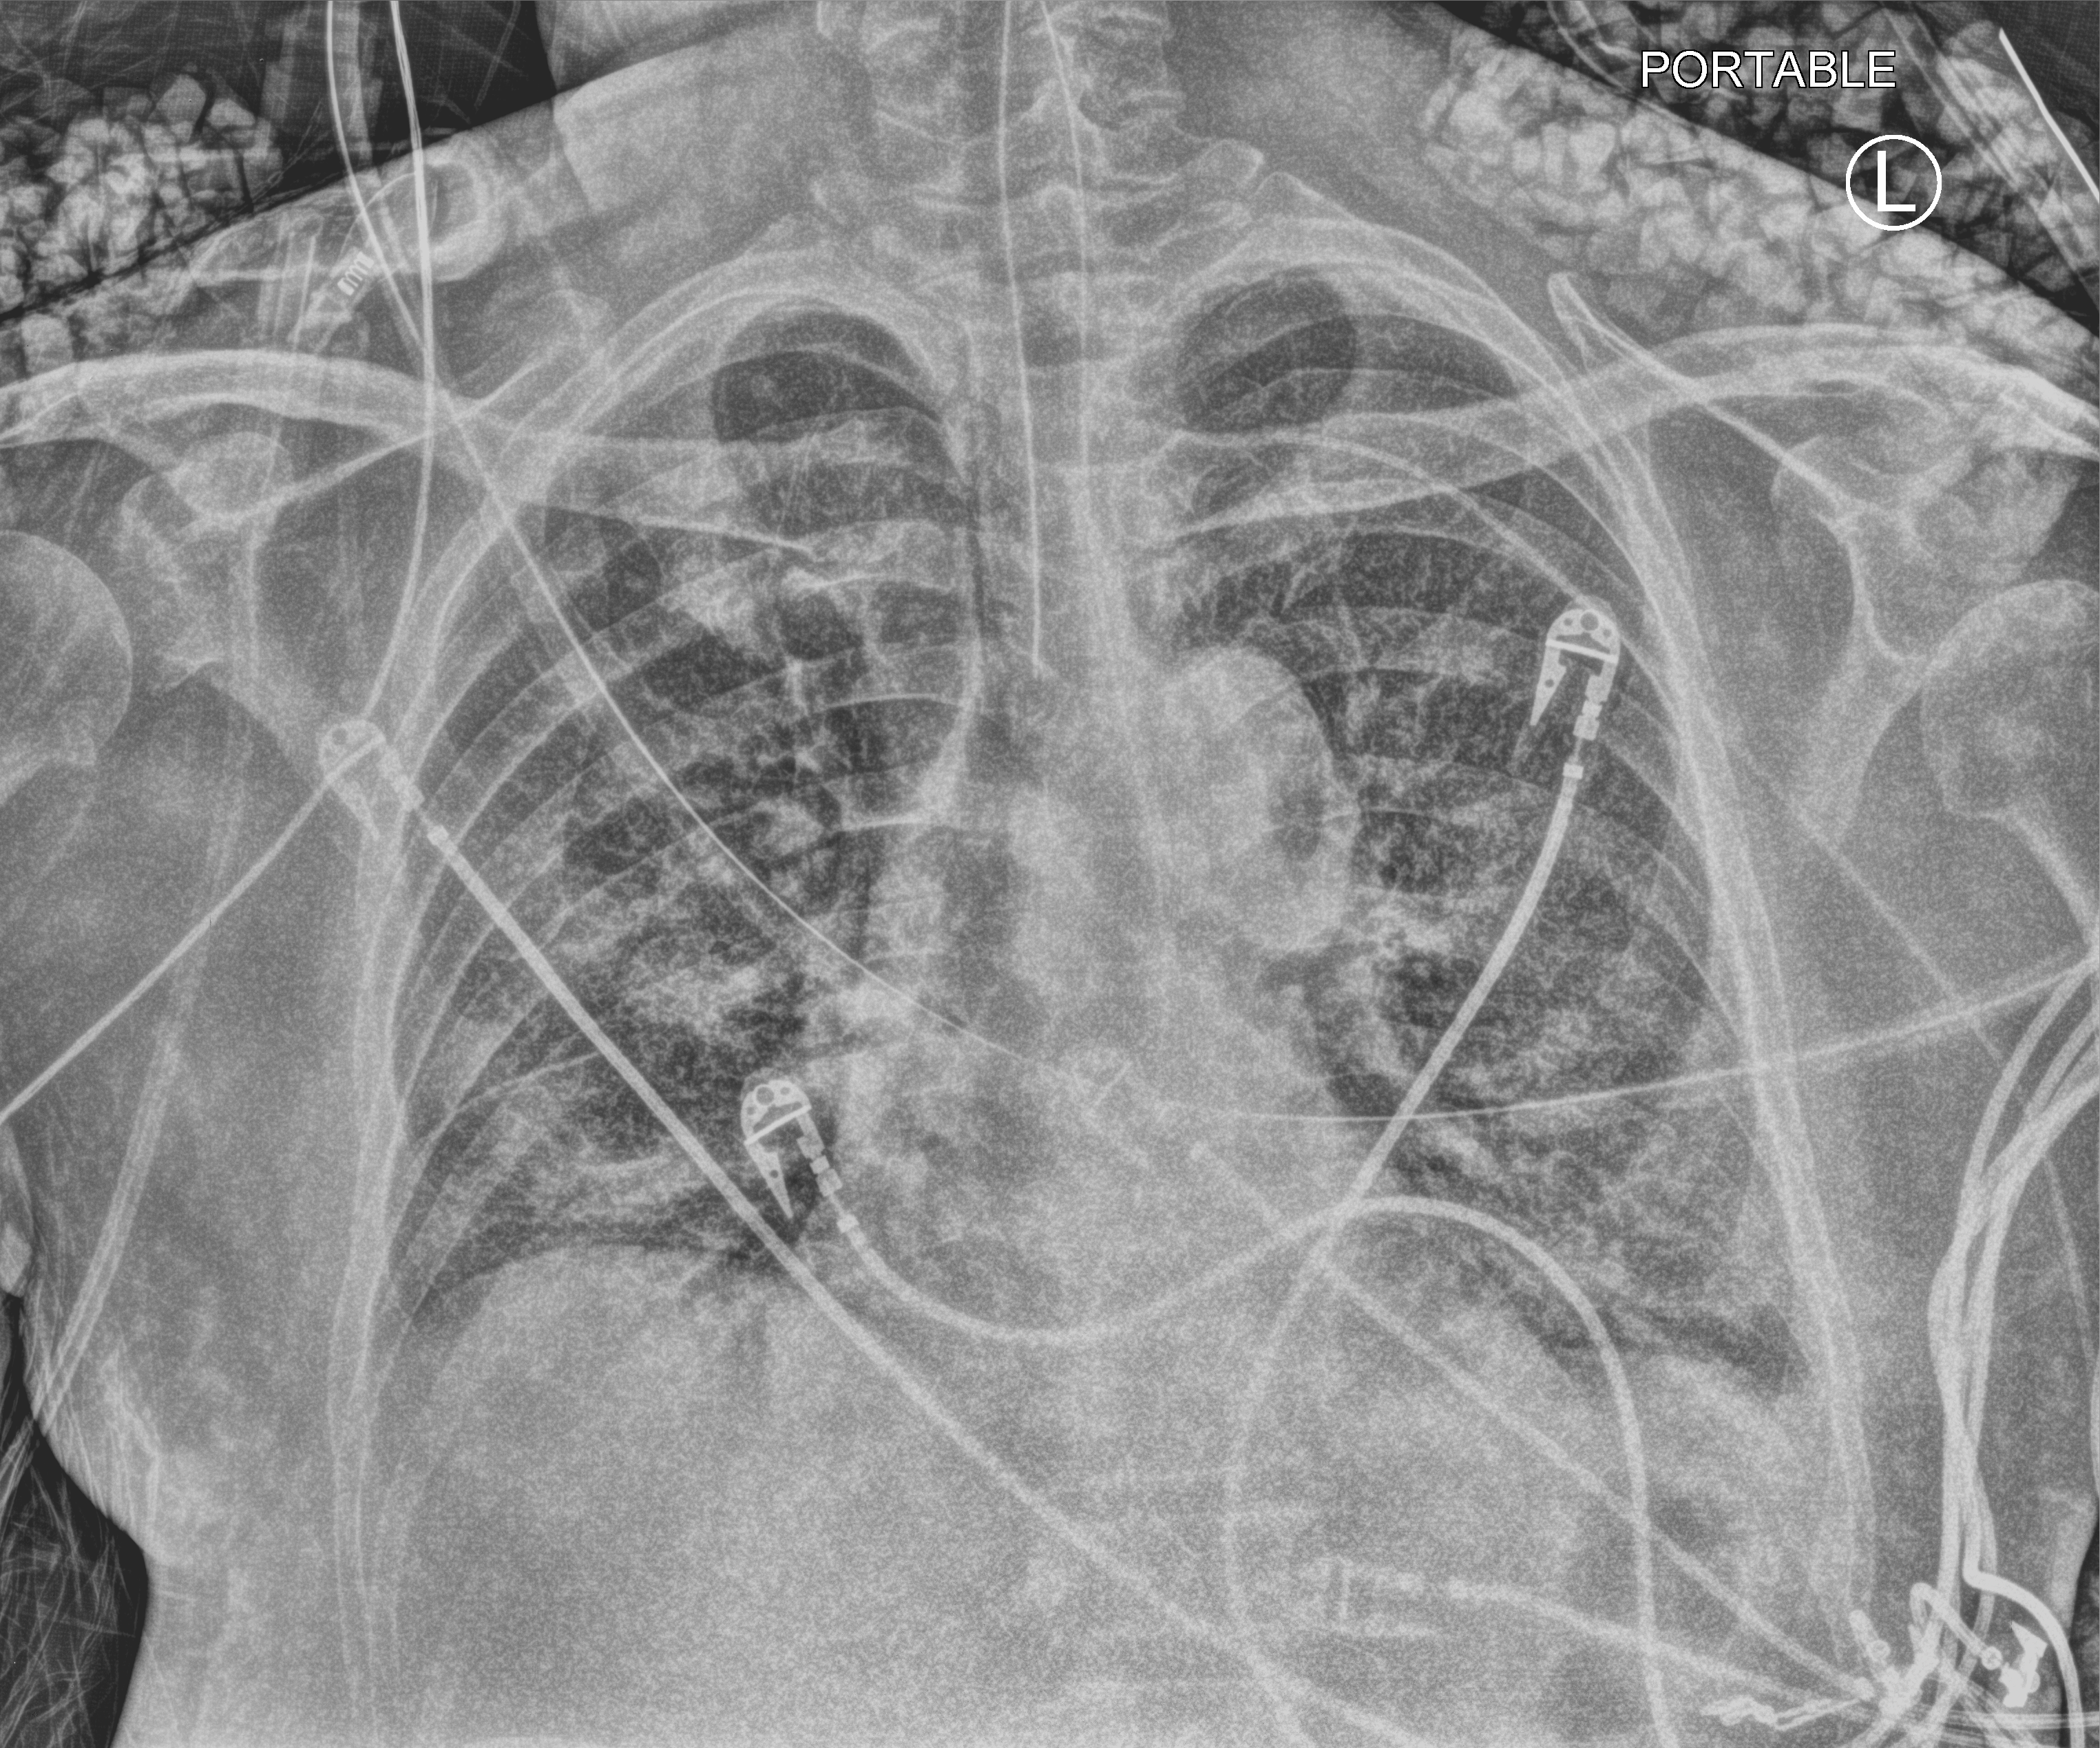
Bedside chest radiograph (computed radiography), anteroposterior (AP) projection. Patient hospitalised with COVID-19; male, aged 60–74 years.
Hospital-stay facts (about this admission, not read from this image; timing relative to this image not recorded):
- mechanically ventilated during this hospital stay: yes